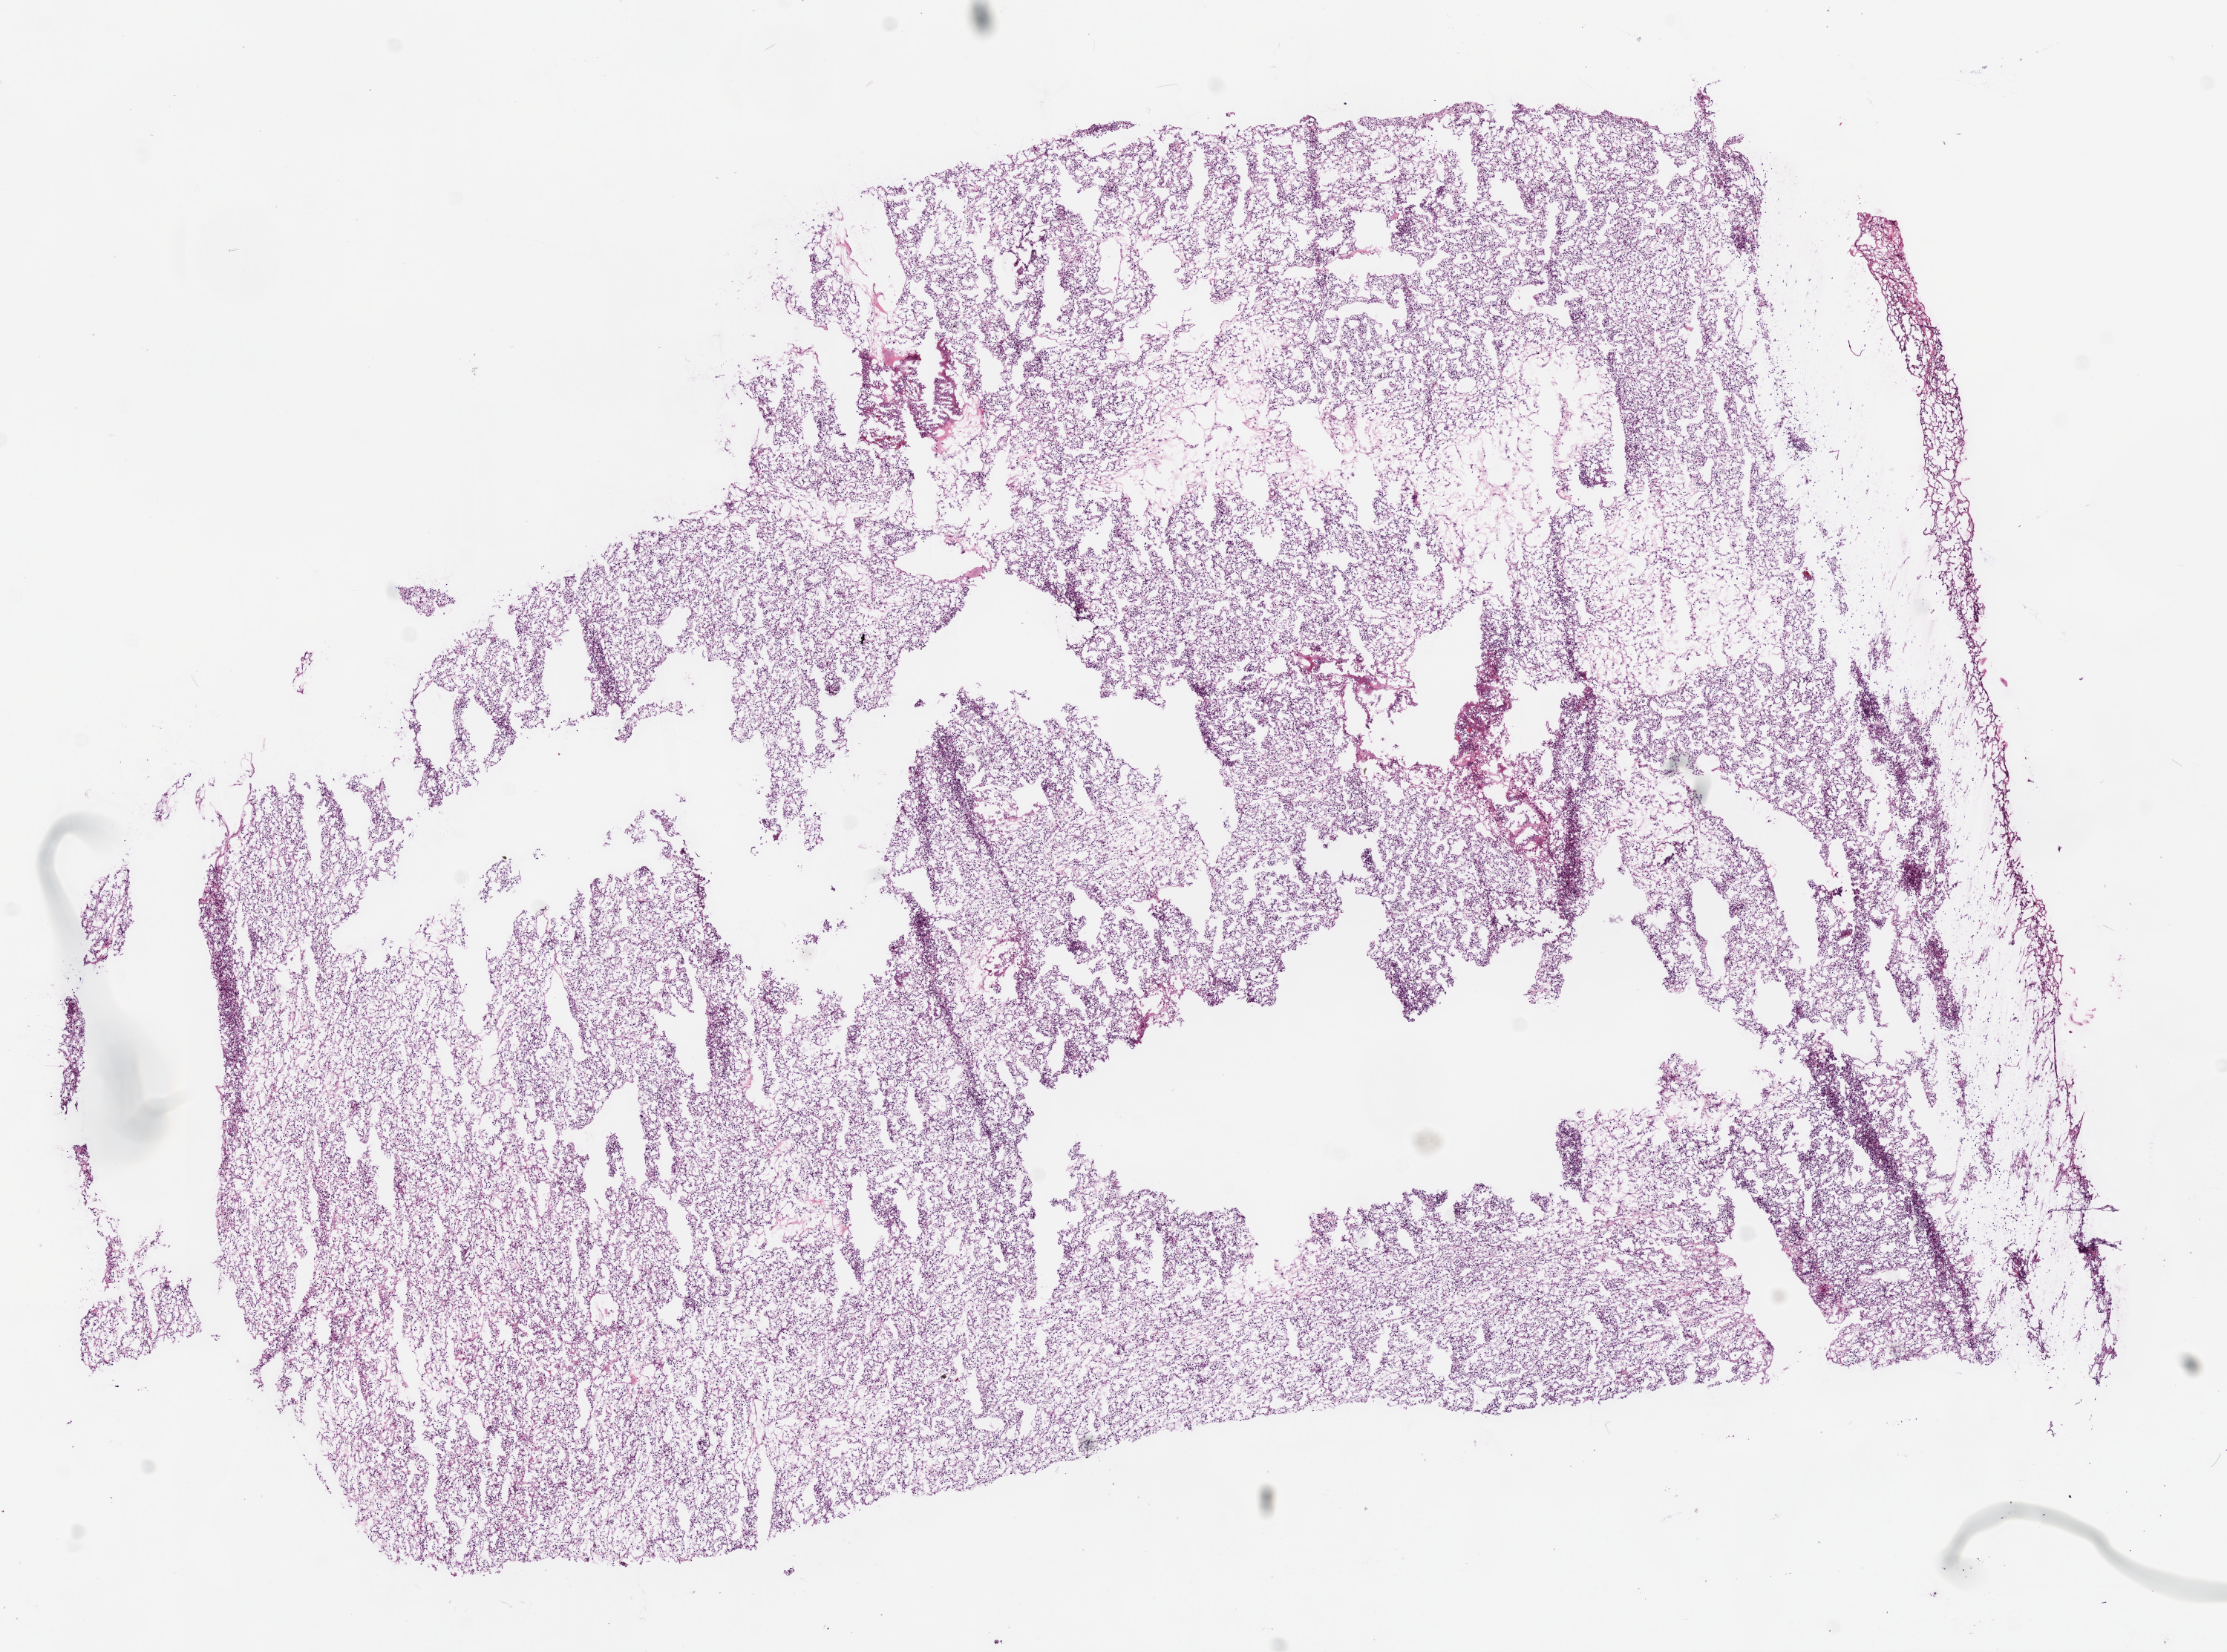
Whole-slide histology image, H&E-stained, a low-resolution overview of the entire scanned area, about 12.0 x 8.9 mm (acquisition: 20x scan). Frozen section. Kidney, primary tumour sample. Patient: male, age at initial diagnosis 62 years. Pathologist review of this section (percent, as recorded): tumour cells 93%, tumour nuclei 75%.
Diagnosis: Clear cell adenocarcinoma, NOS.